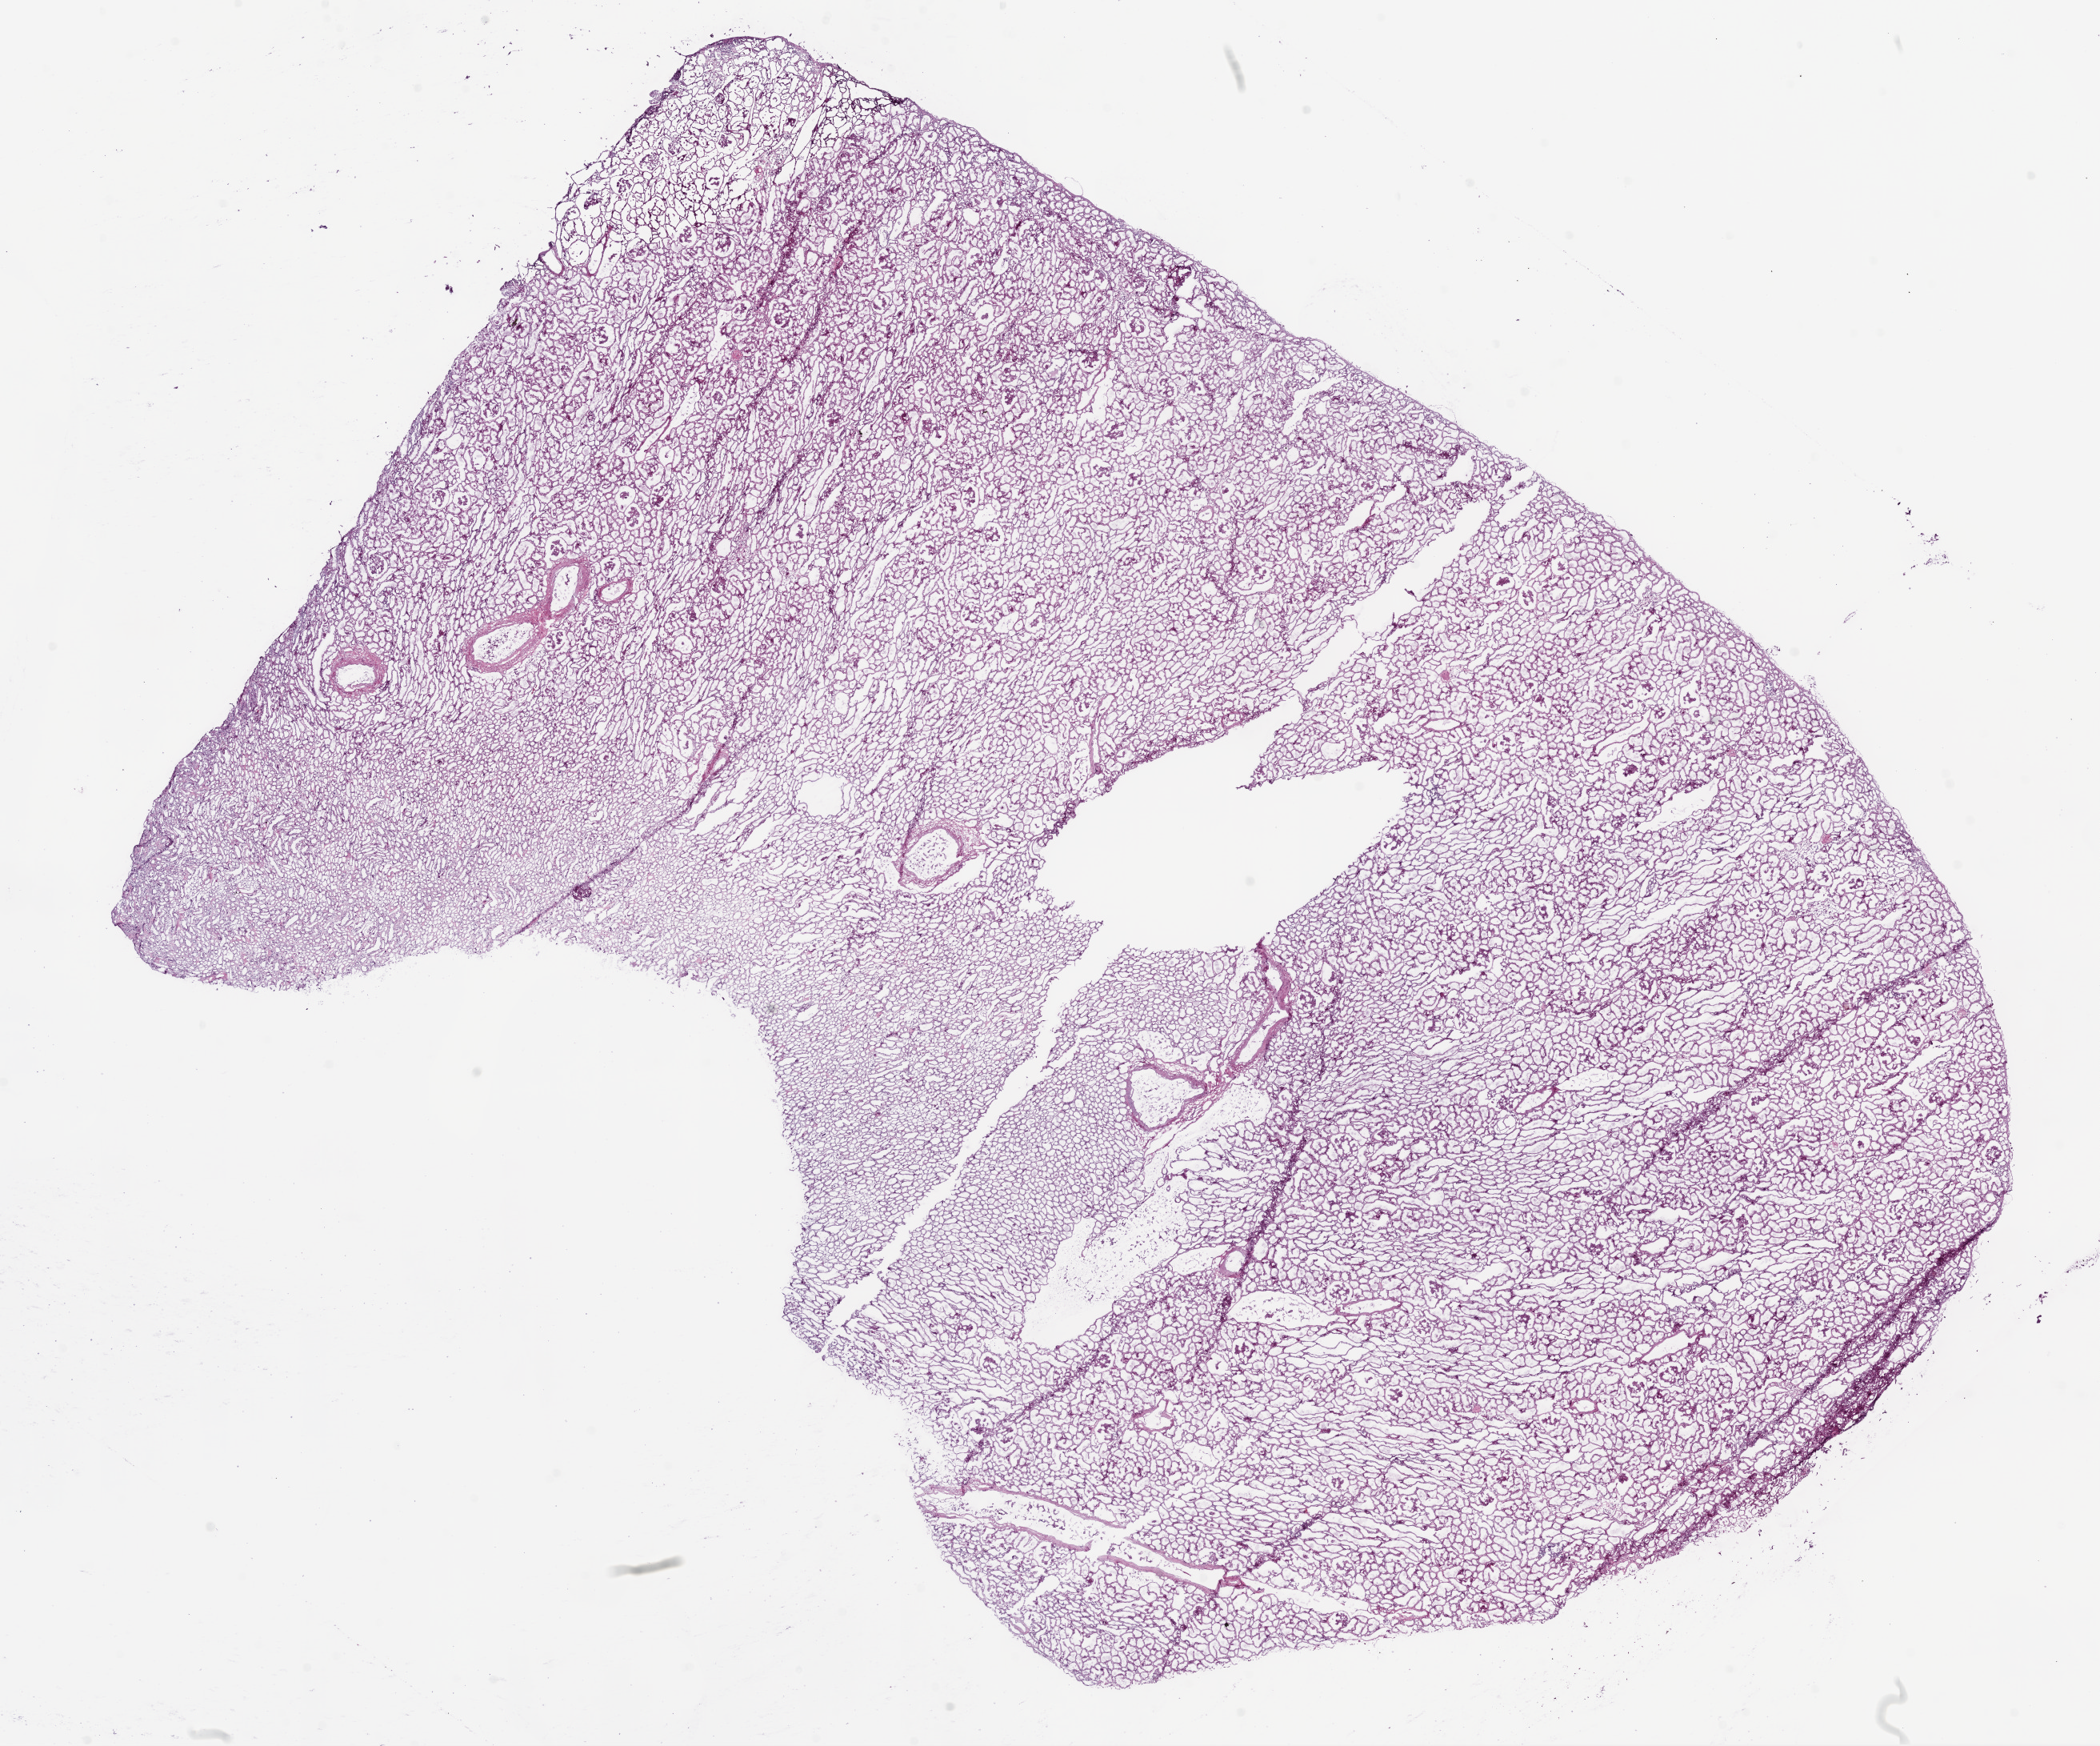
H&E whole-slide image, whole scanned area (about 21.1 x 17.5 mm, from a 20x scan) shown as a low-resolution overview. Frozen section from the bottom of the tissue portion. Sample: solid tissue normal (non-tumour tissue), kidney. Patient: male, age at initial diagnosis 56 years.
• this section: solid tissue normal (non-tumour) sample from the same patient
• patient diagnosis: Clear cell adenocarcinoma, NOS